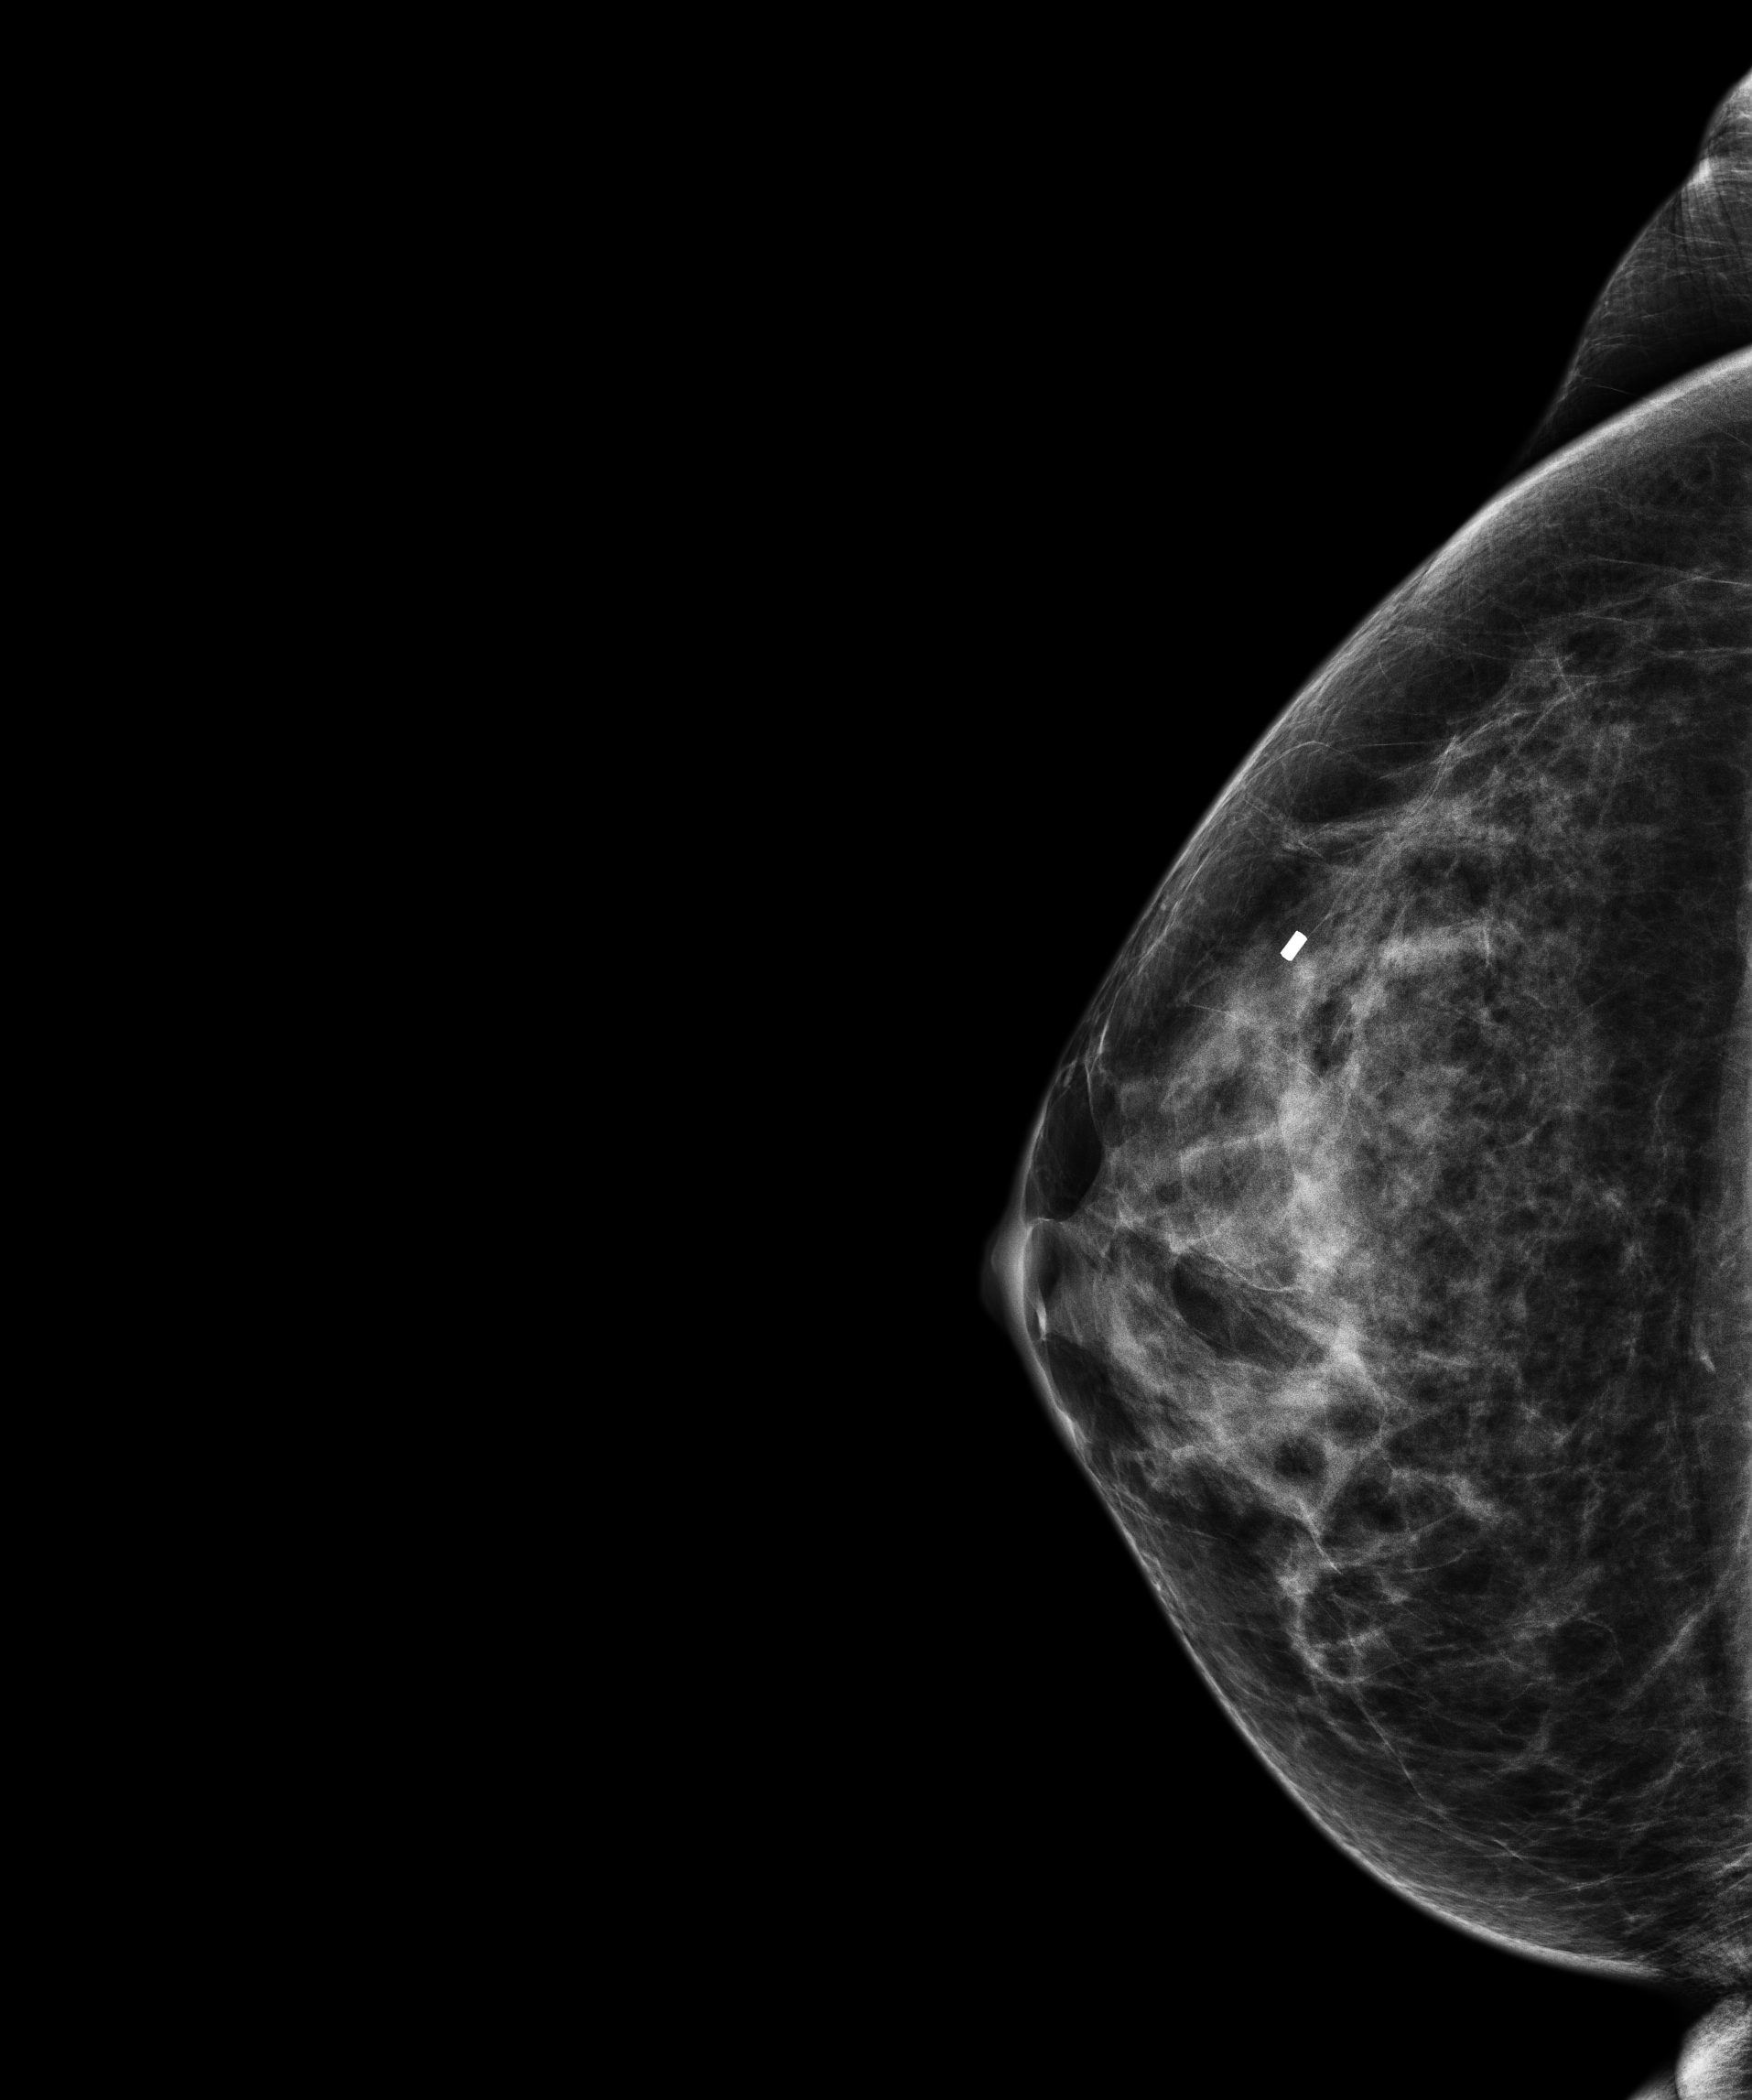
Annual screening mammography examination, compressed breast thickness 54.3 mm, system: Senographe Pristina. Patient aged 43 years (female).
Image type: full-field digital mammogram. Breast: right. Projection: cranio-caudal projection.